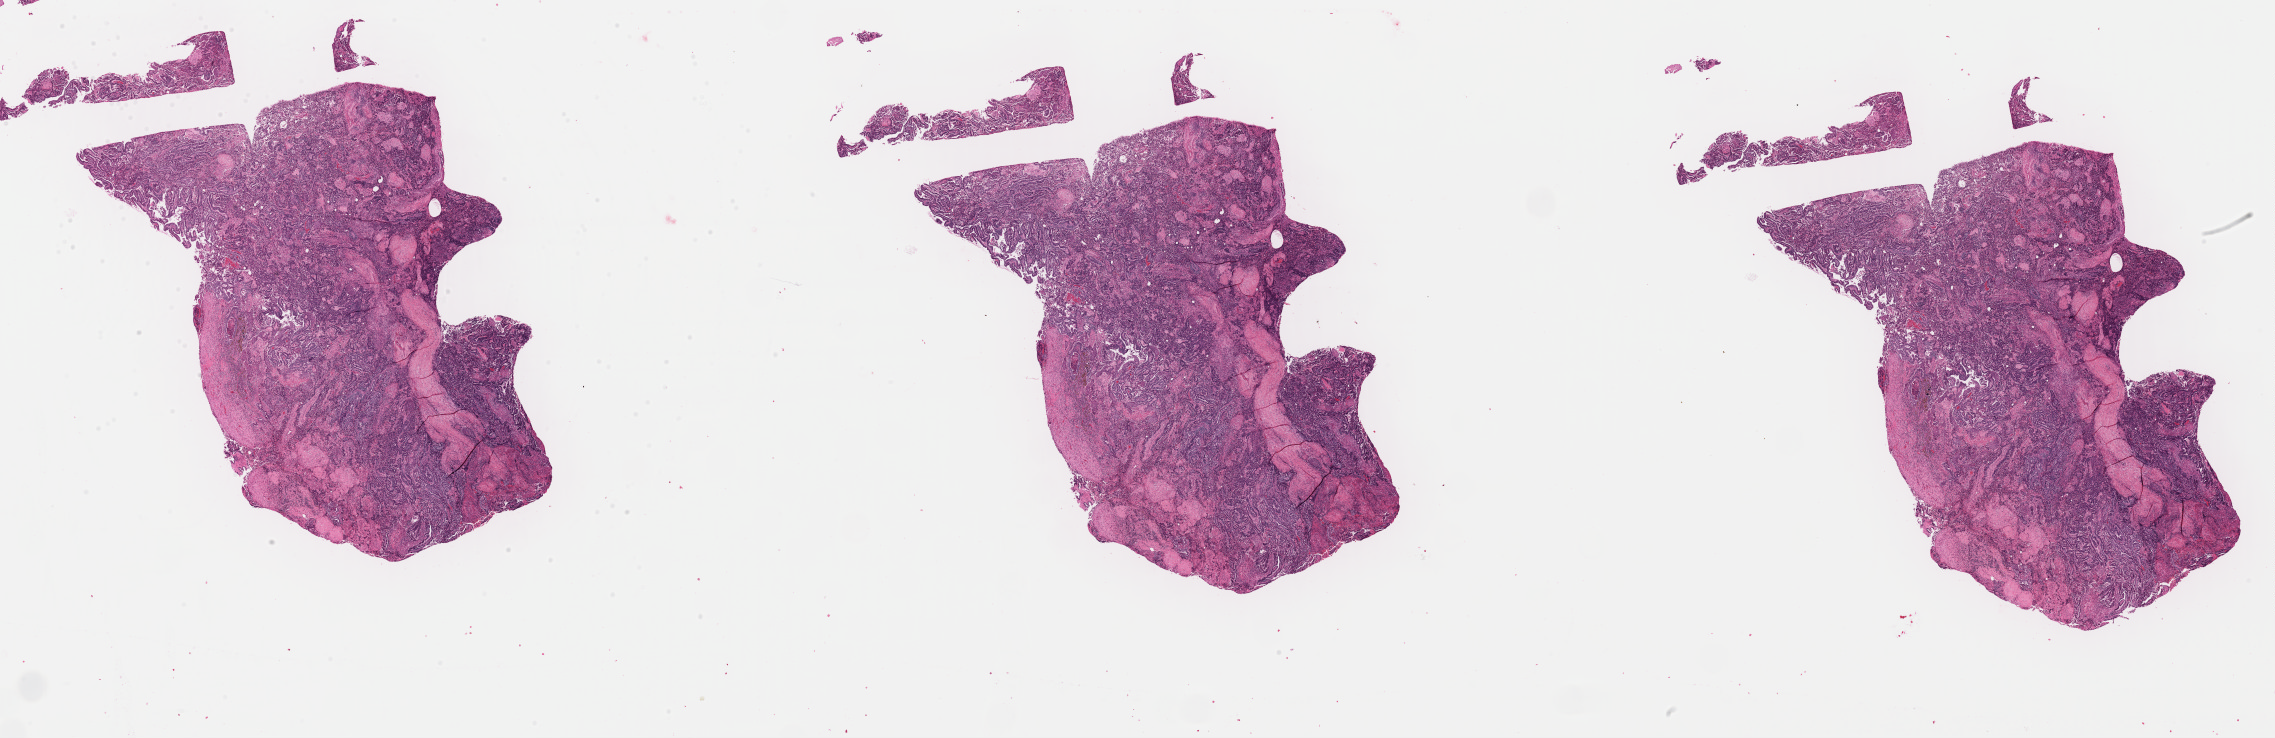
H&E-stained whole-slide image — low-resolution overview of the scanned area, about 35.9 x 11.7 mm (acquisition: 40x scan), FFPE section, uterus, primary tumour sample. Female, age 54 years at initial diagnosis. Histologic grade: G1 (well differentiated).
* pathologic diagnosis: Endometrioid adenocarcinoma, NOS
* FIGO stage: IA